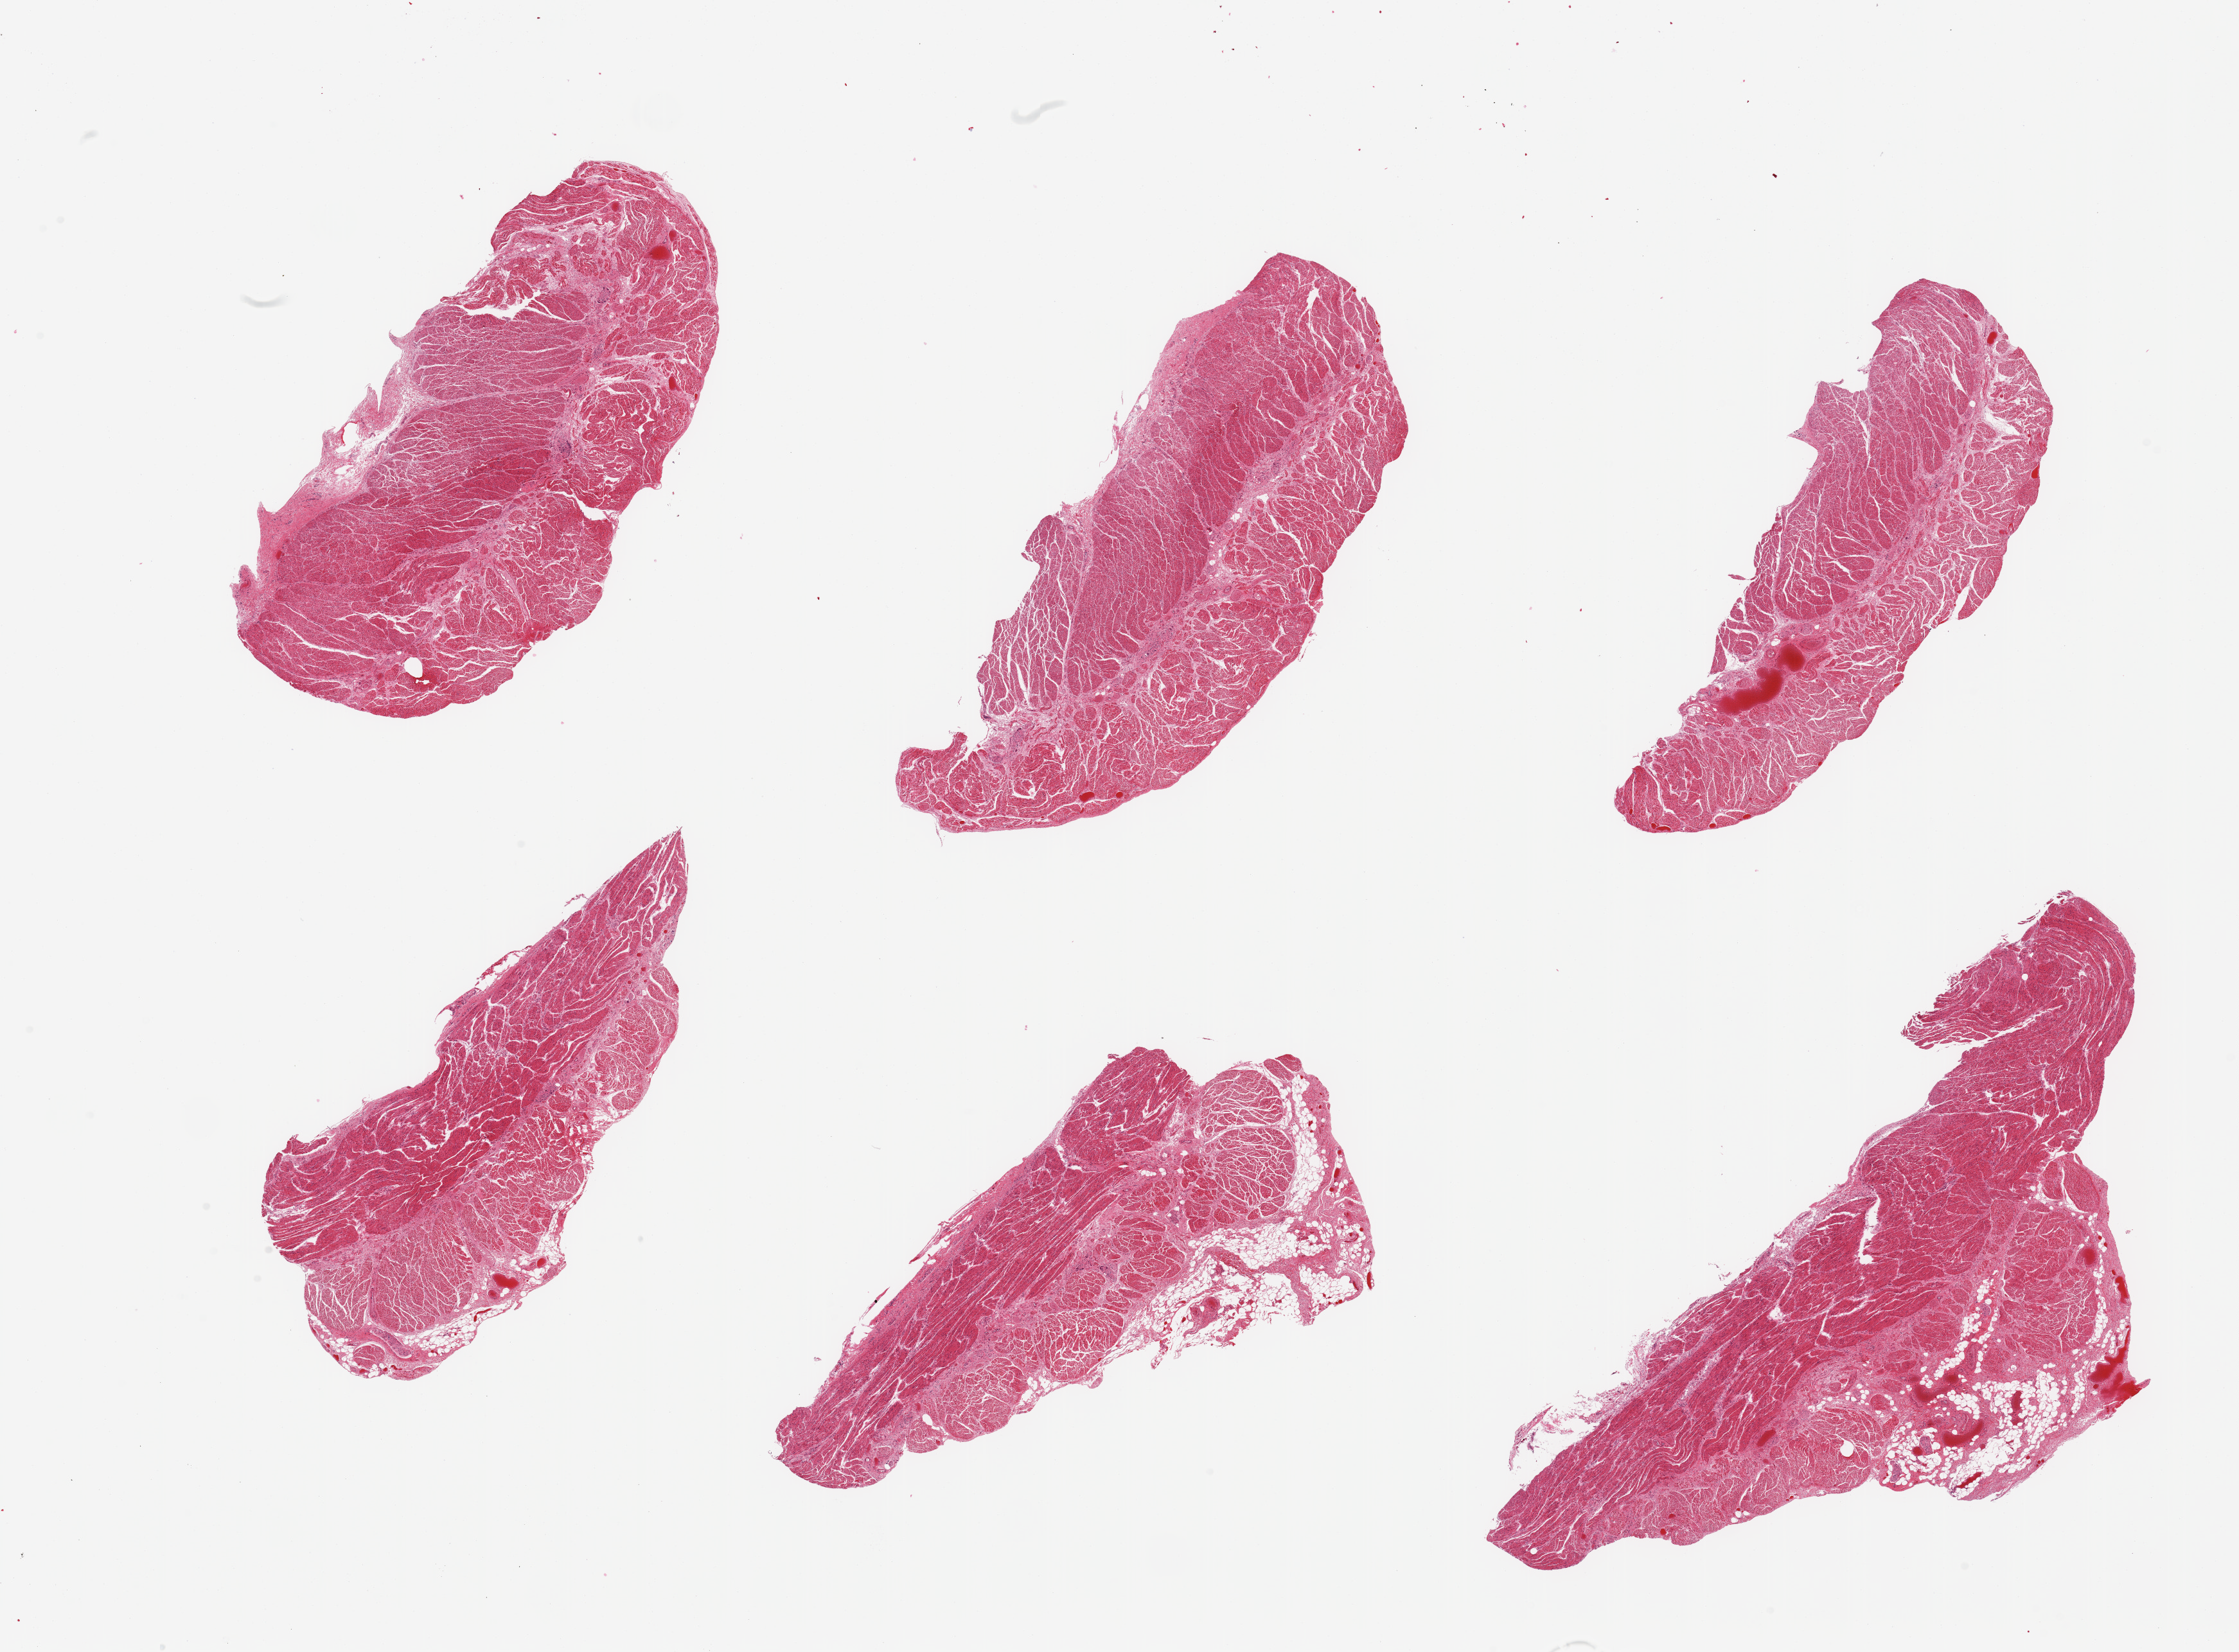
Digitized hematoxylin and eosin (H&E)-stained section, brightfield — a low-resolution overview of the entire scanned area, about 27.6 x 20.3 mm (slide scanned at 20x), PAXgene-fixed paraffin-embedded (PFPE) section, target tissue: gastroesophageal junction, tissue donor sample. Donor sex: male.
• pathologist's review note for this sample: 6 pieces, confirmed target muscularis, adhrent nubbins of fat up to ~1mm